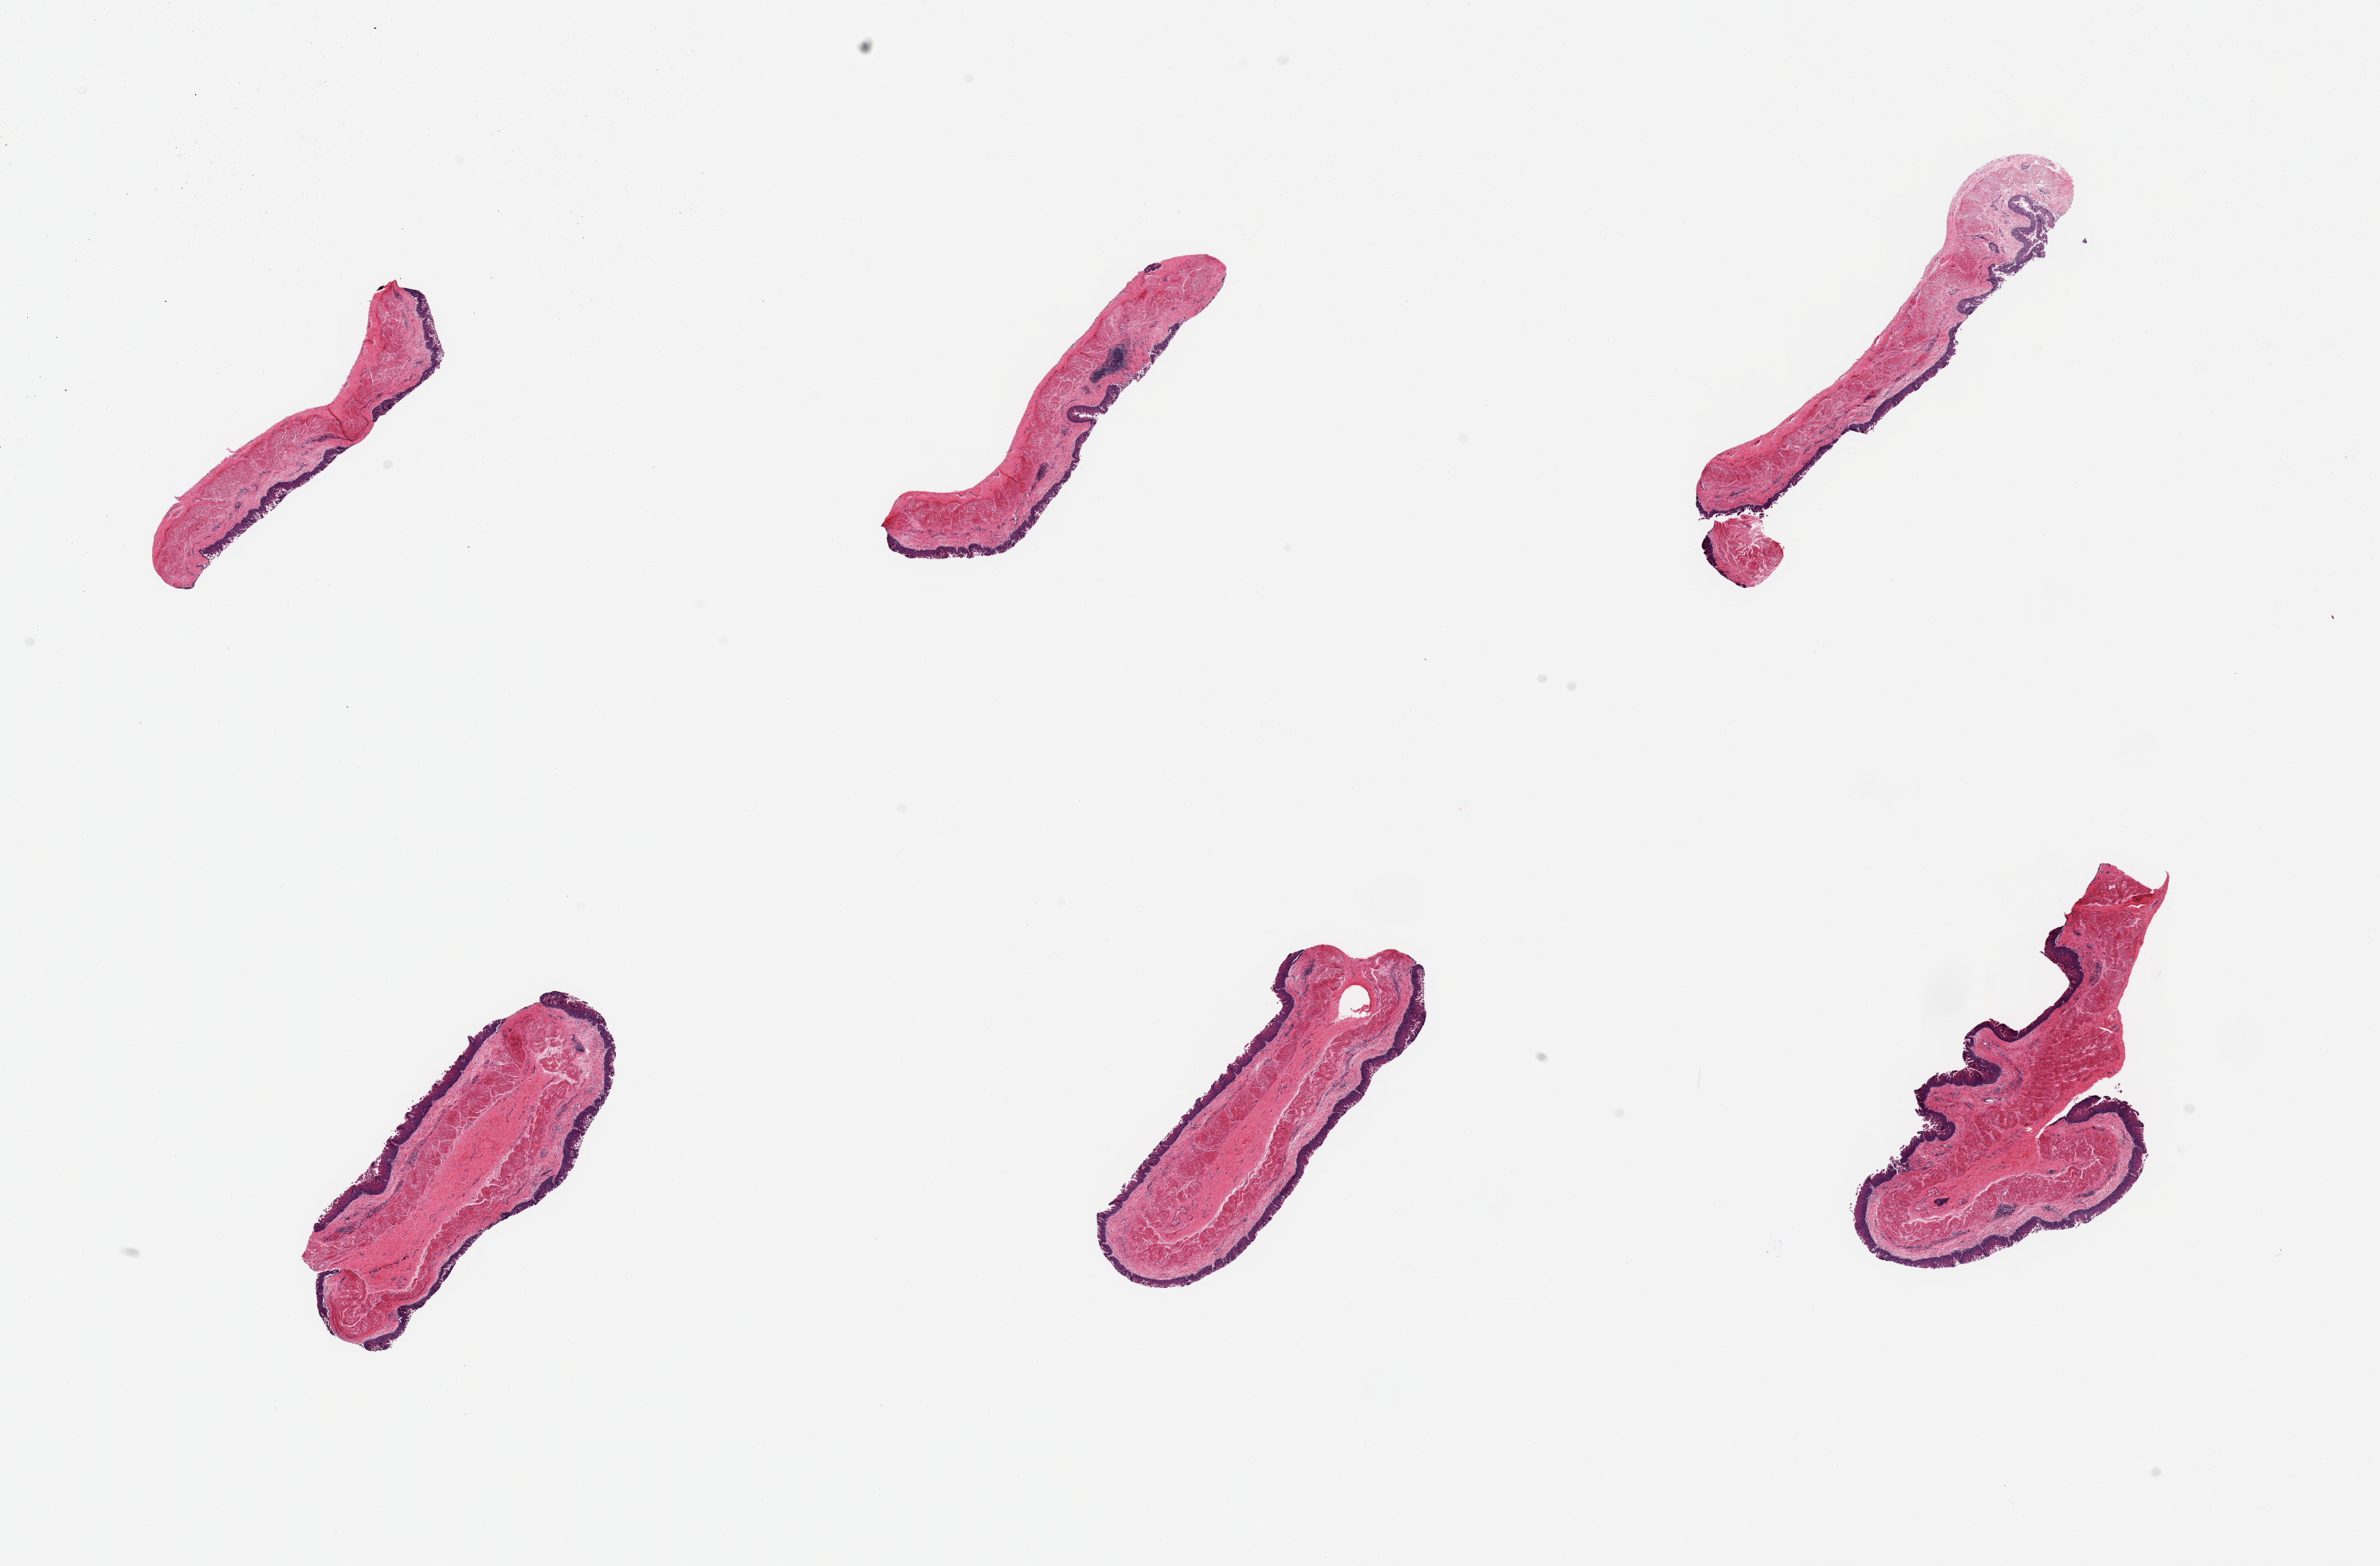
Digitized hematoxylin and eosin (H&E)-stained section — whole scanned area (about 23.6 x 15.6 mm) shown as a low-resolution overview; PAXgene-fixed paraffin-embedded (PFPE) section; sampled site (target tissue): esophageal mucous membrane; tissue donor sample. Donor sex: female.
Reviewer comment on this tissue sample: 6 pieces; epithelium partially sloughed.